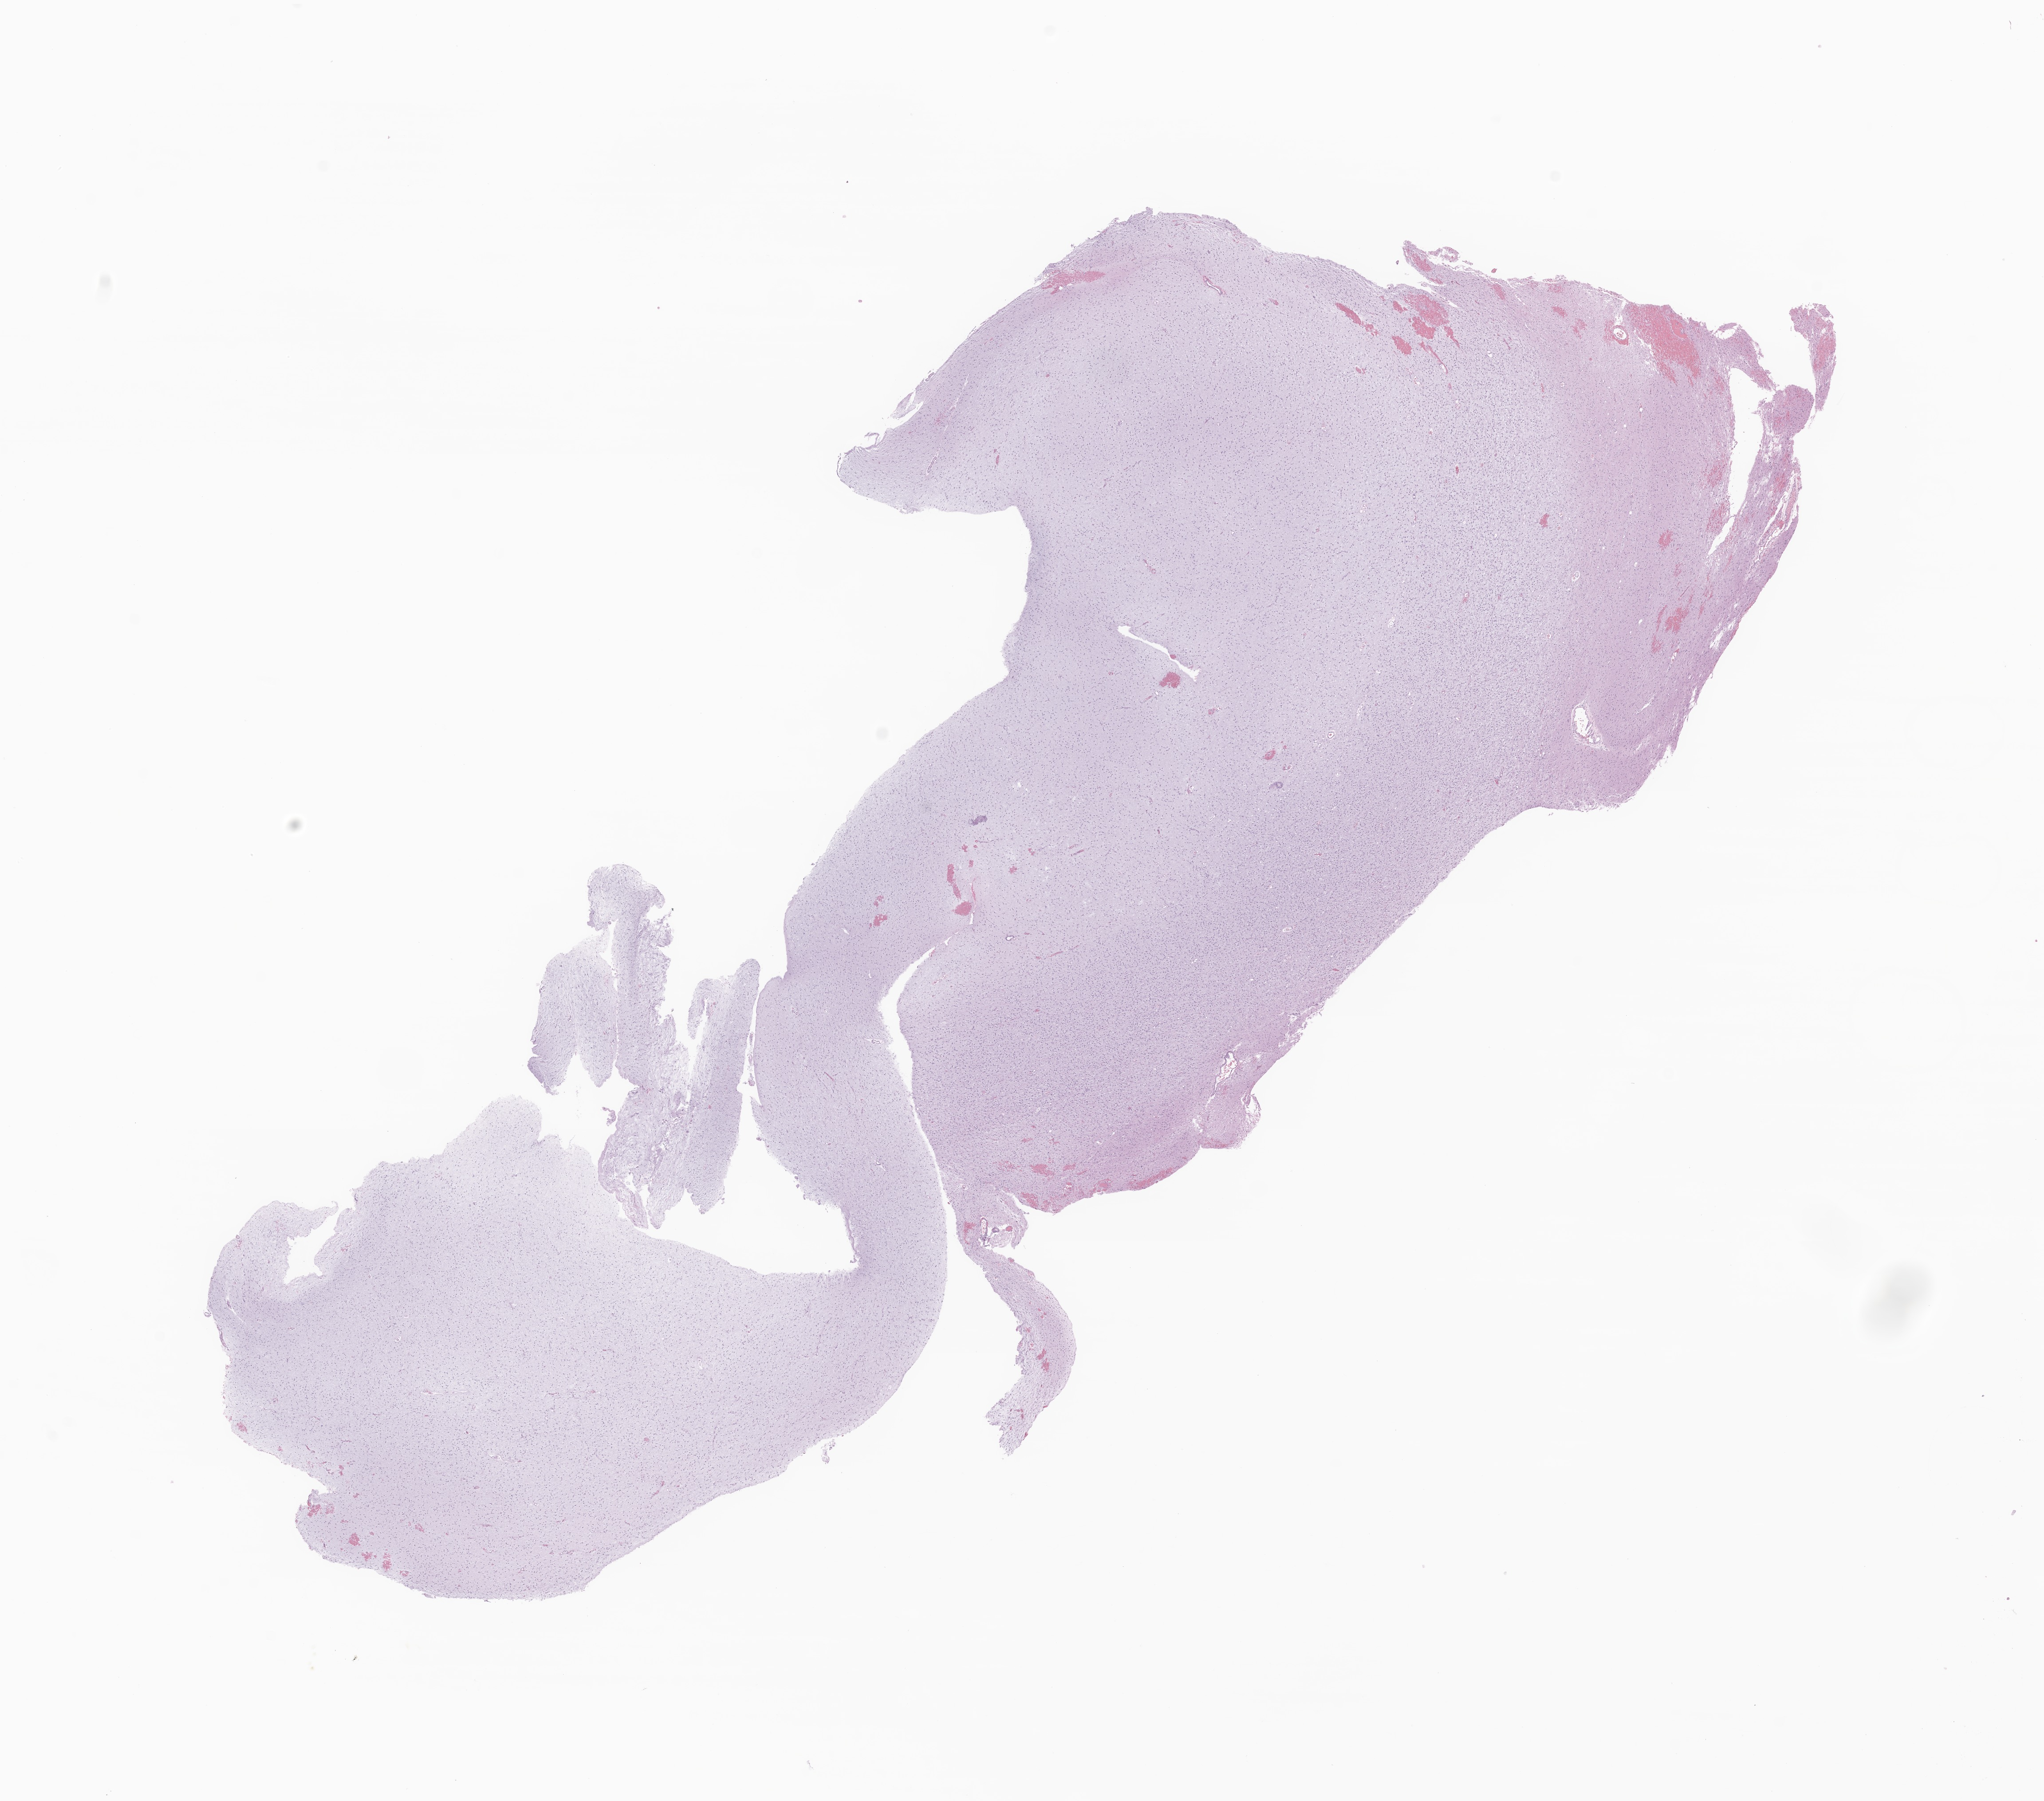
H&E whole-slide image of tumor tissue from the cerebral ventricle — whole scanned area (about 19.4 x 17.1 mm) shown as a low-resolution overview. Formalin-fixed paraffin-embedded section. Patient: male, age 844 days.
Diagnosis: Oligoastrocytoma, NOS.